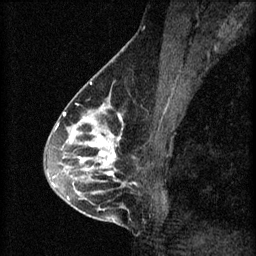
Breast MRI (dynamic contrast-enhanced), one sagittal slice; position 32 of 60 along the scan axis; 3 images stored at this slice position (order not interpretable as contrast timing); 1.5 T; TE 4.2 ms, TR 8.2 ms; 2 mm slice thickness; 256 × 256 image matrix, field of view 180 × 180 mm. Patient: female, 45 years.
Annotated regions visible in this slice (semi-automatically segmented with operator editing):
- analysis volume of interest (the breast-tissue region the enhancement analysis was run in; not a lesion): bounding box (x1, y1, x2, y2) in pixels: (54, 104, 159, 217)
- tumour enhancement mask (voxels above the 70 % enhancement threshold inside the analysis volume of interest): (54, 104, 125, 203)